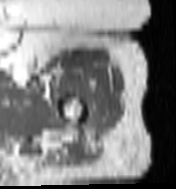
MRI of an extremity soft-tissue mass, one axial slice. Position 95 of 100 along the scan axis. MR volume resampled by the dataset authors to the PET/CT grid (not the native acquisition matrix). 3.27 mm slice thickness. 176 × 189 image matrix. Female patient. Case-level facts recorded for this patient, not image findings: histological type: undifferentiated – high grade; grade: high; site of the primary tumour: left thigh.
Structures marked on this image (expert contour drawn on MRI and transferred to this co-registered scan by the dataset authors):
- gross tumour volume including surrounding oedema: bounding box [x1, y1, x2, y2] px = [94, 112, 99, 117]